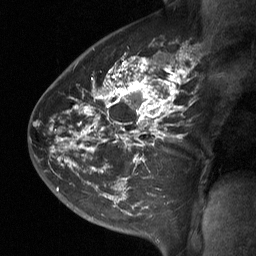
Breast MRI (dynamic contrast-enhanced), one sagittal slice. Slice 43 of 64 in the series (ordered by position). Dynamic contrast-enhanced study with each time point stored as its own series, time point 2 of 3 at this slice position (early post-contrast, ordered by acquisition time). 1.5 T. TE 4.8 ms, TR 27 ms. 2 mm slice thickness. 256 × 256 image matrix, field of view 200 × 200 mm. Patient: female, 42 years. Case-level facts recorded for this patient, not image findings: setting: breast cancer imaged before/during neoadjuvant chemotherapy; receptor status: triple-negative.
Annotated regions visible in this slice (semi-automatic segmentation, software-assisted and operator-edited):
- analysis volume of interest (the breast-tissue region the enhancement analysis was run in; not a lesion): bounding box (x1, y1, x2, y2) in pixels: (49, 45, 192, 197)
- tumour enhancement mask (voxels above the 90 % enhancement threshold inside the analysis volume of interest): (52, 52, 189, 165)